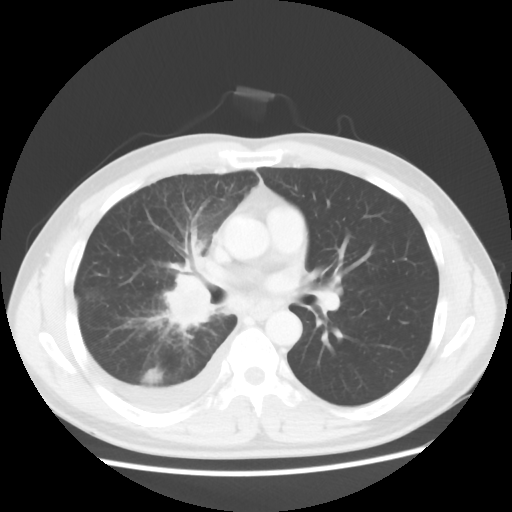
Chest CT, one axial slice. Position 30 of 56 along the scan axis. Reconstruction kernel STANDARD. Lung window (W 1500 / L -600 HU). 5 mm slice thickness. 512 × 512 image matrix. Male patient, age 46 years. From the clinical record (not read from this slice): clinical TNM (as recorded): T2 N3 M1.
Outlined on this slice (rectangle marked by the reading radiologist):
- lung tumour (recorded histology: adenocarcinoma): bounding box <157,265,217,339> (left, top, right, bottom; pixels)